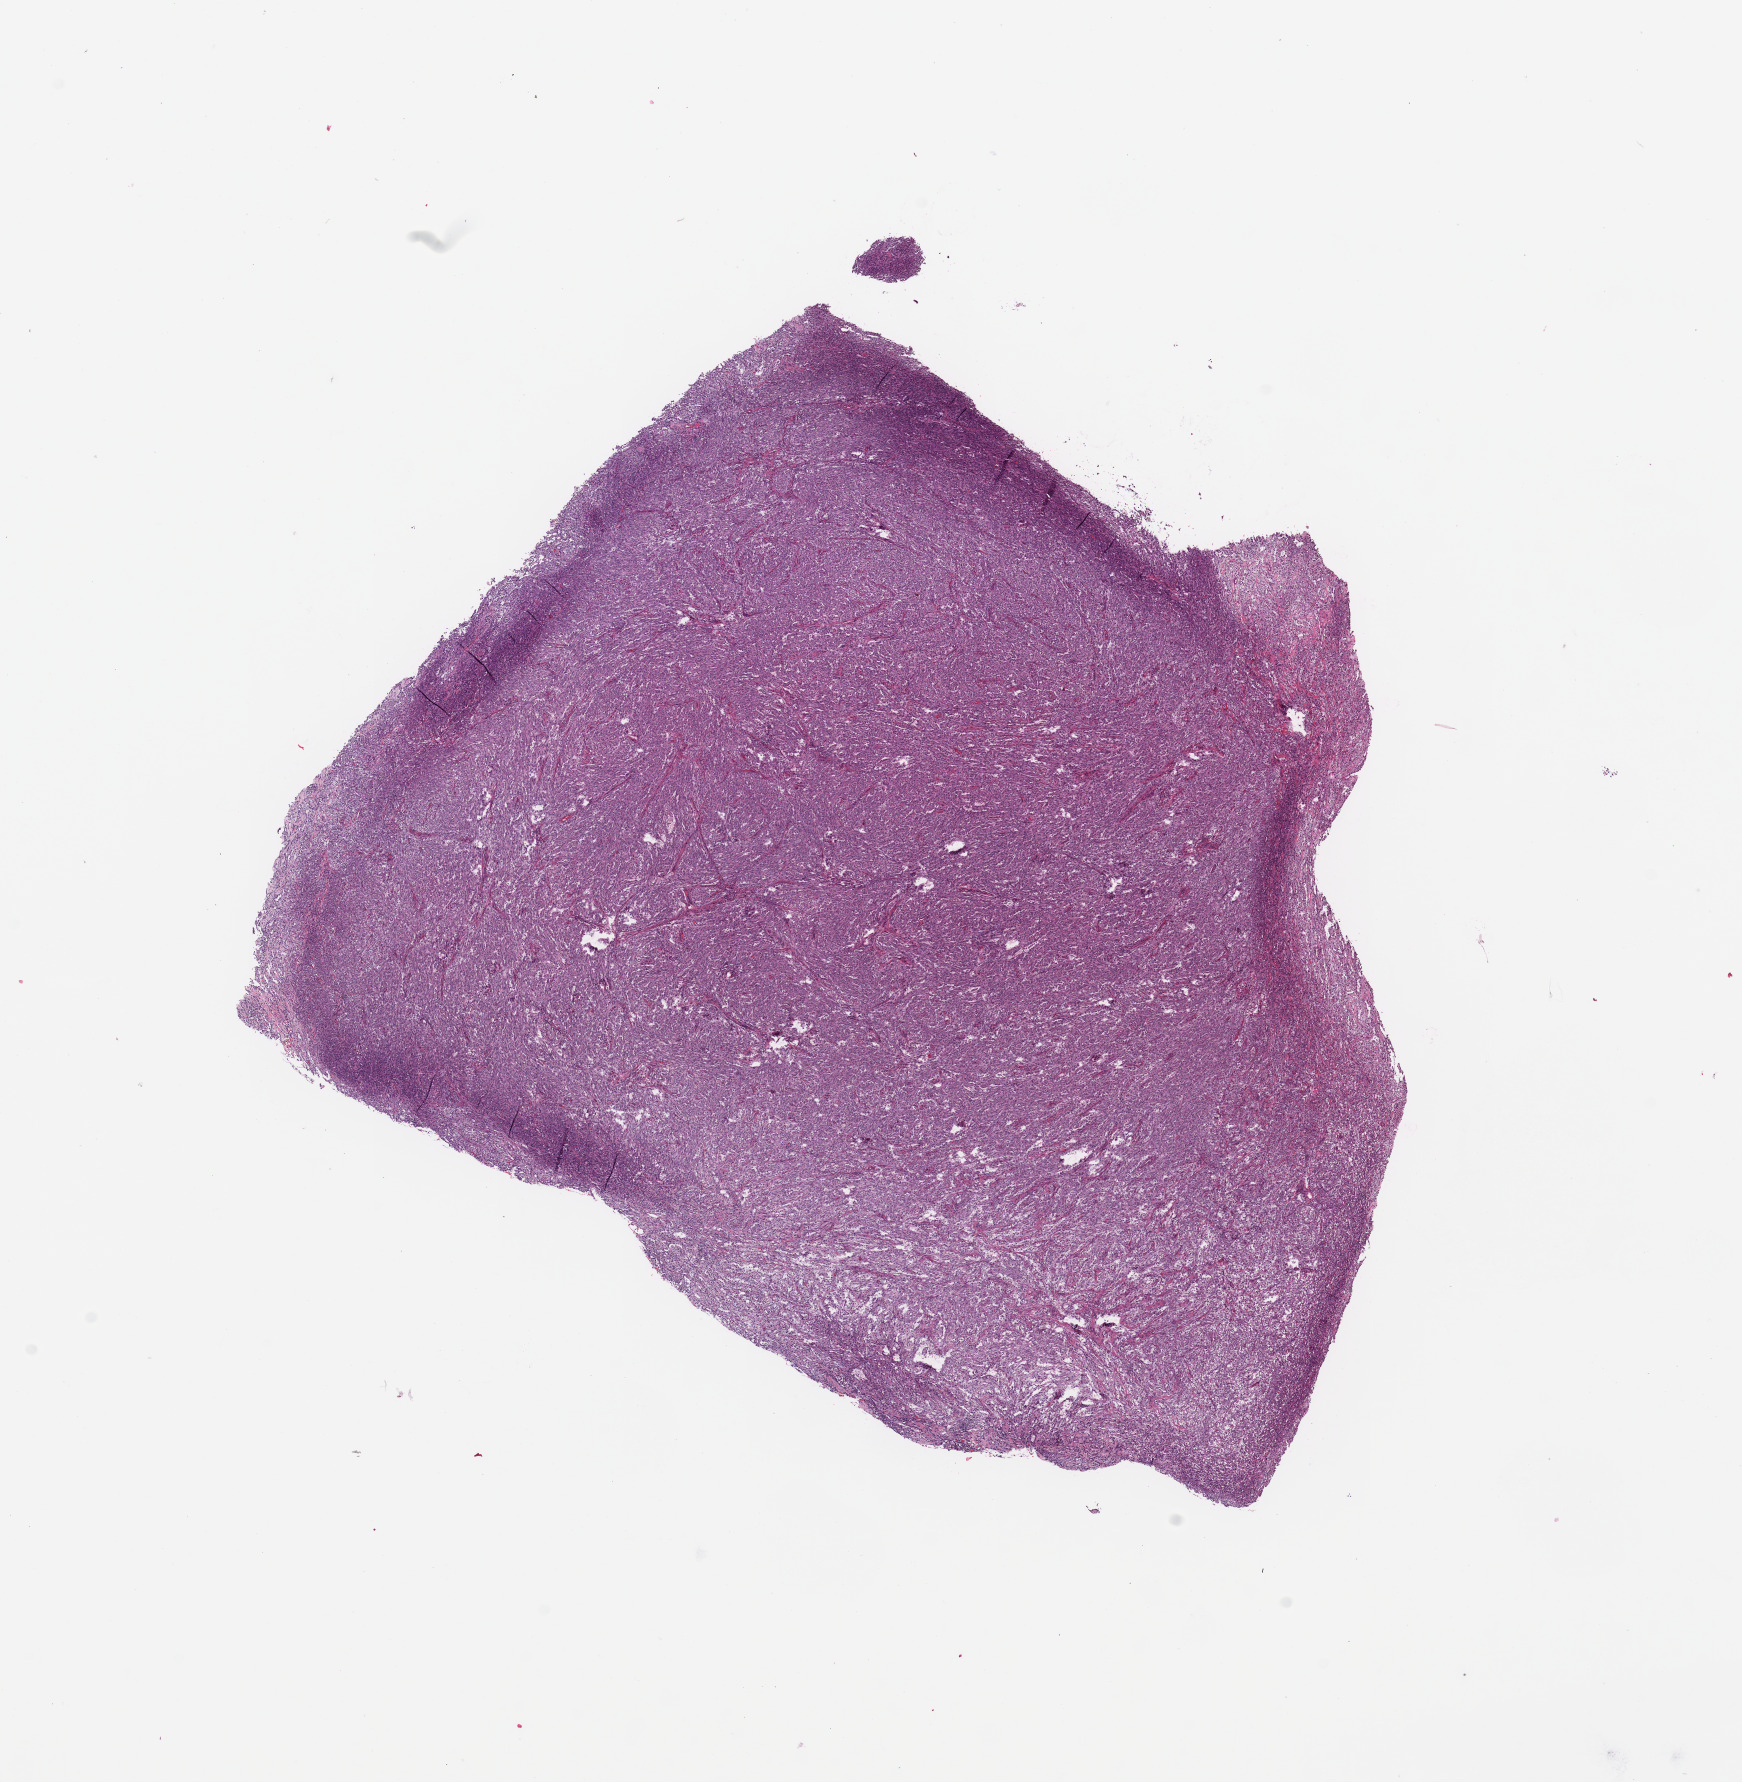
Digitized H&E tissue section (whole slide) — low-resolution overview of the scanned area, about 13.8 x 14.1 mm (from a 20x scan). Tumour tissue sample, sampled site: kidney. 61-year-old male patient. Slide review estimates, as recorded: tumour nuclei 90%, necrosis 2%.
Histologic diagnosis: Renal cell carcinoma, NOS.